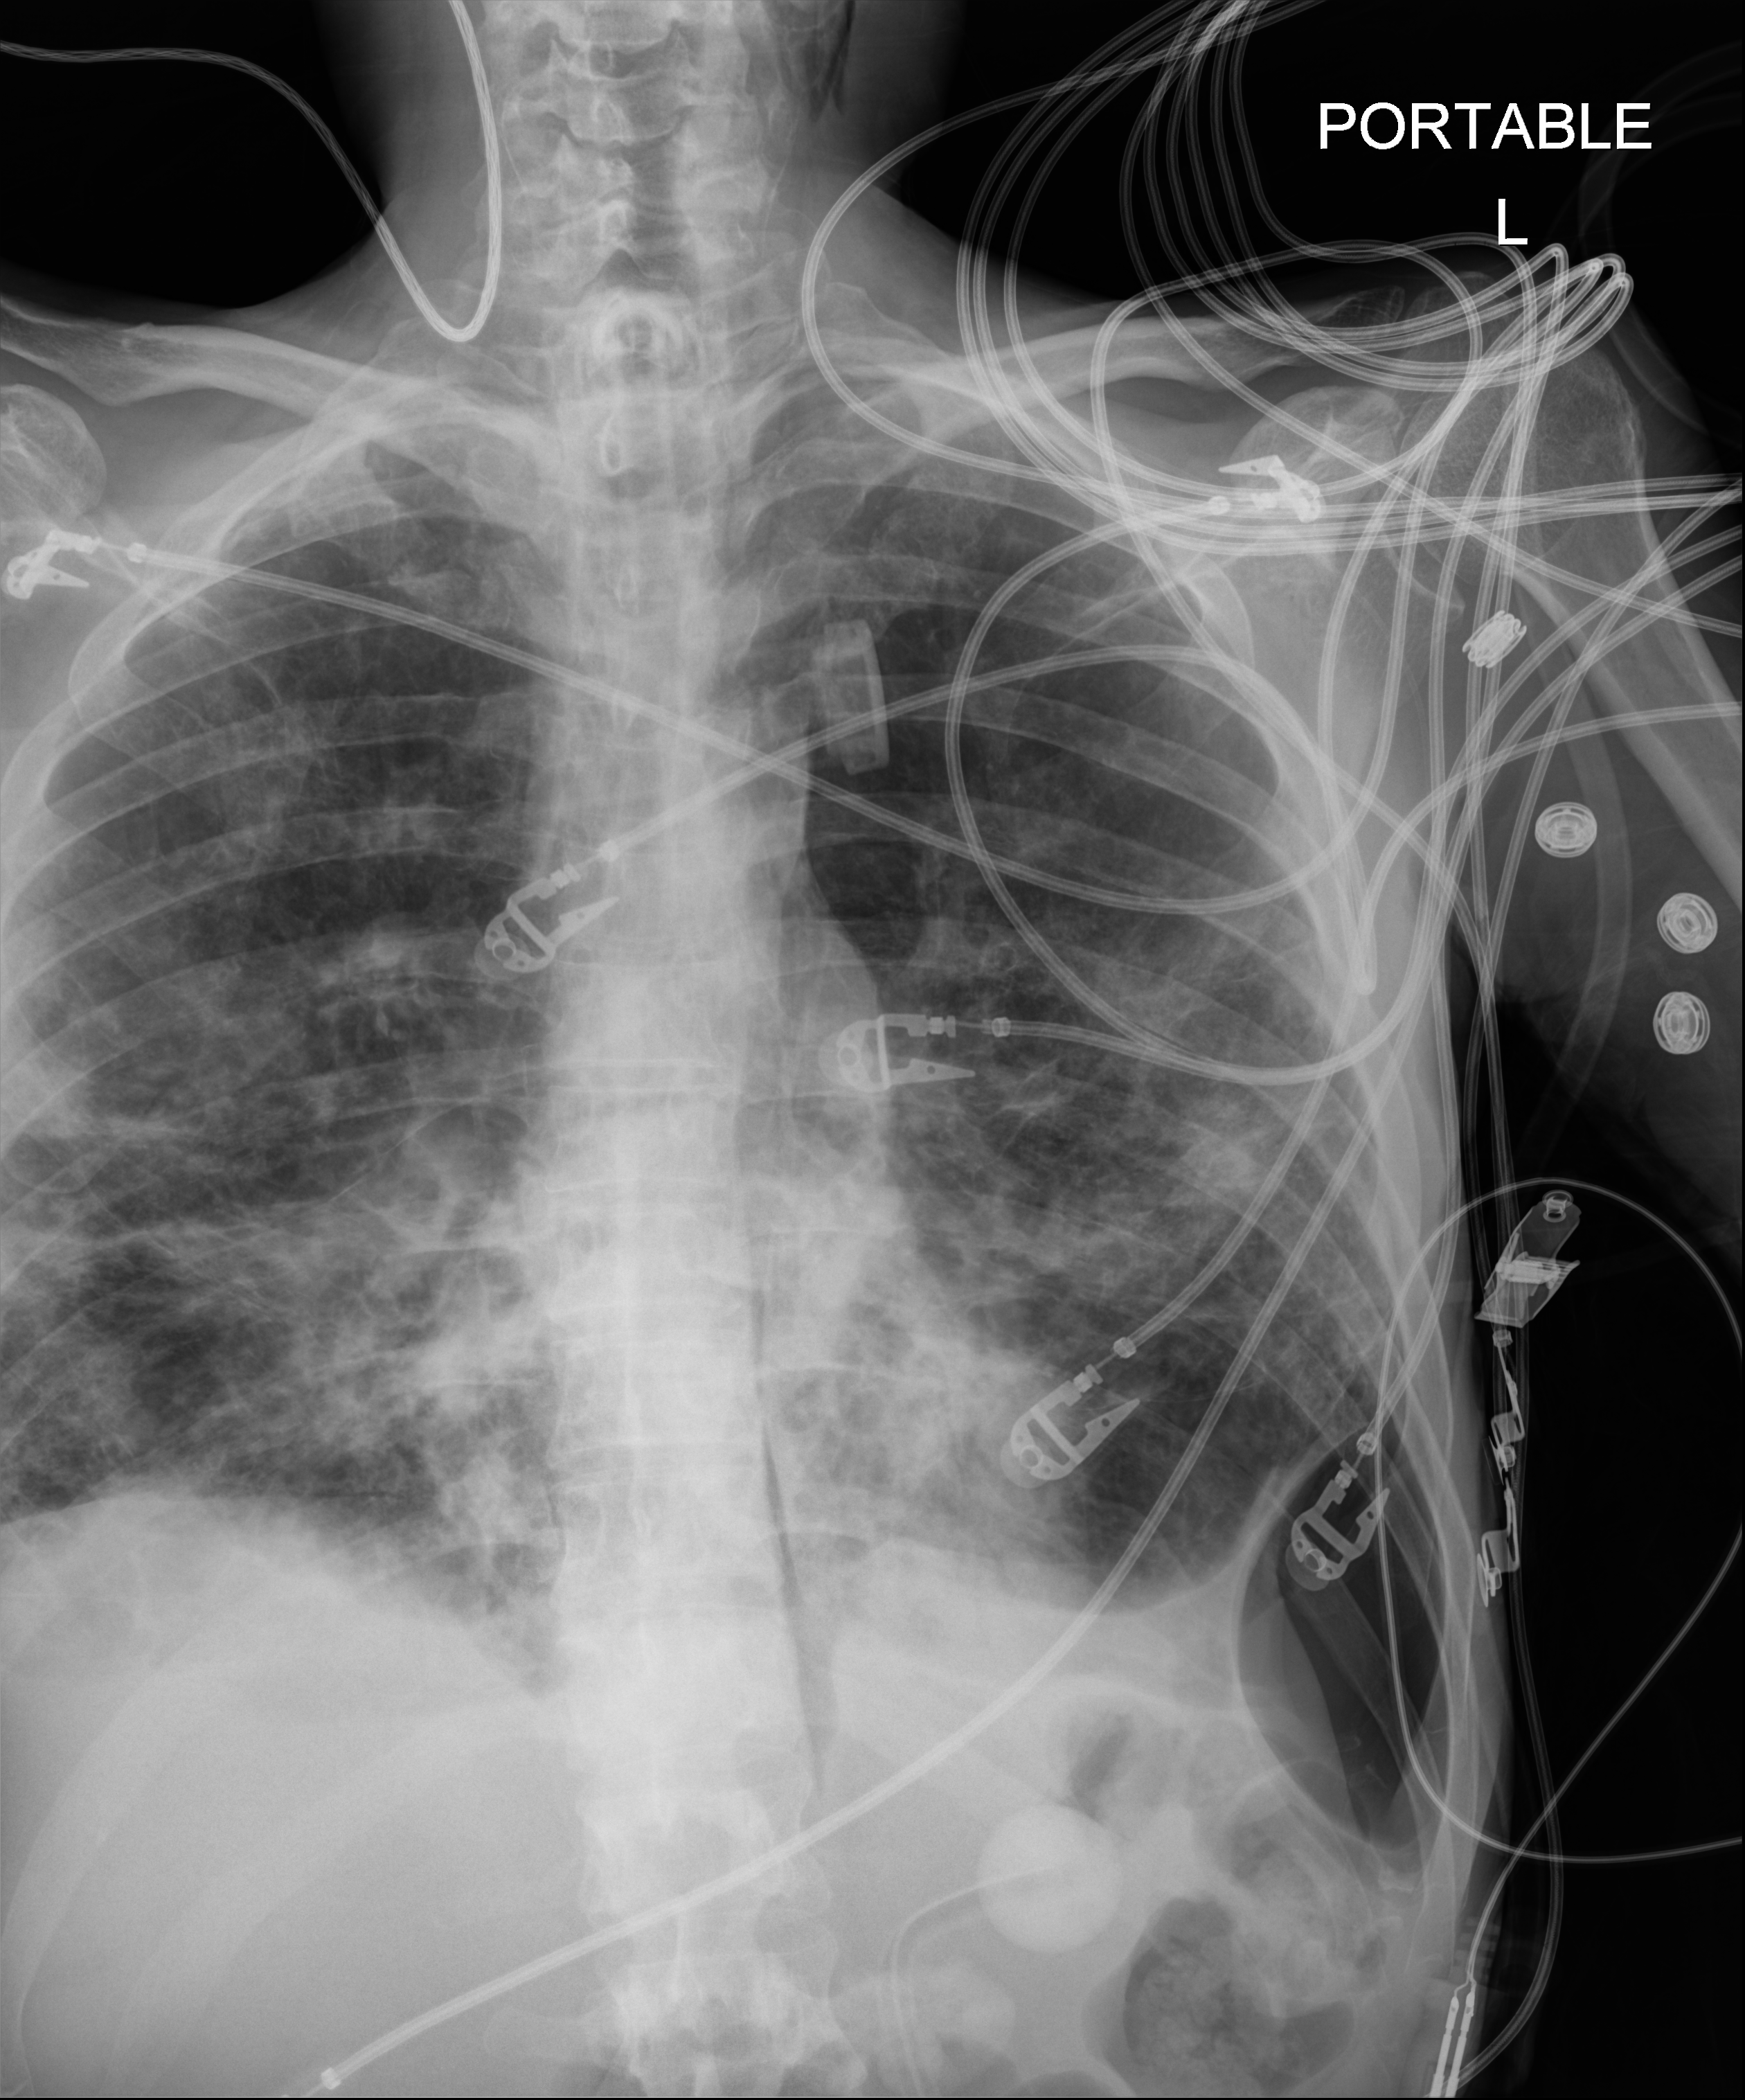
Chest radiograph. Patient hospitalised with COVID-19; male, aged 18–59 years.
From the hospital-stay record, not from the radiograph (when in the stay this image was taken is not recorded): mechanically ventilated during this hospital stay: yes.